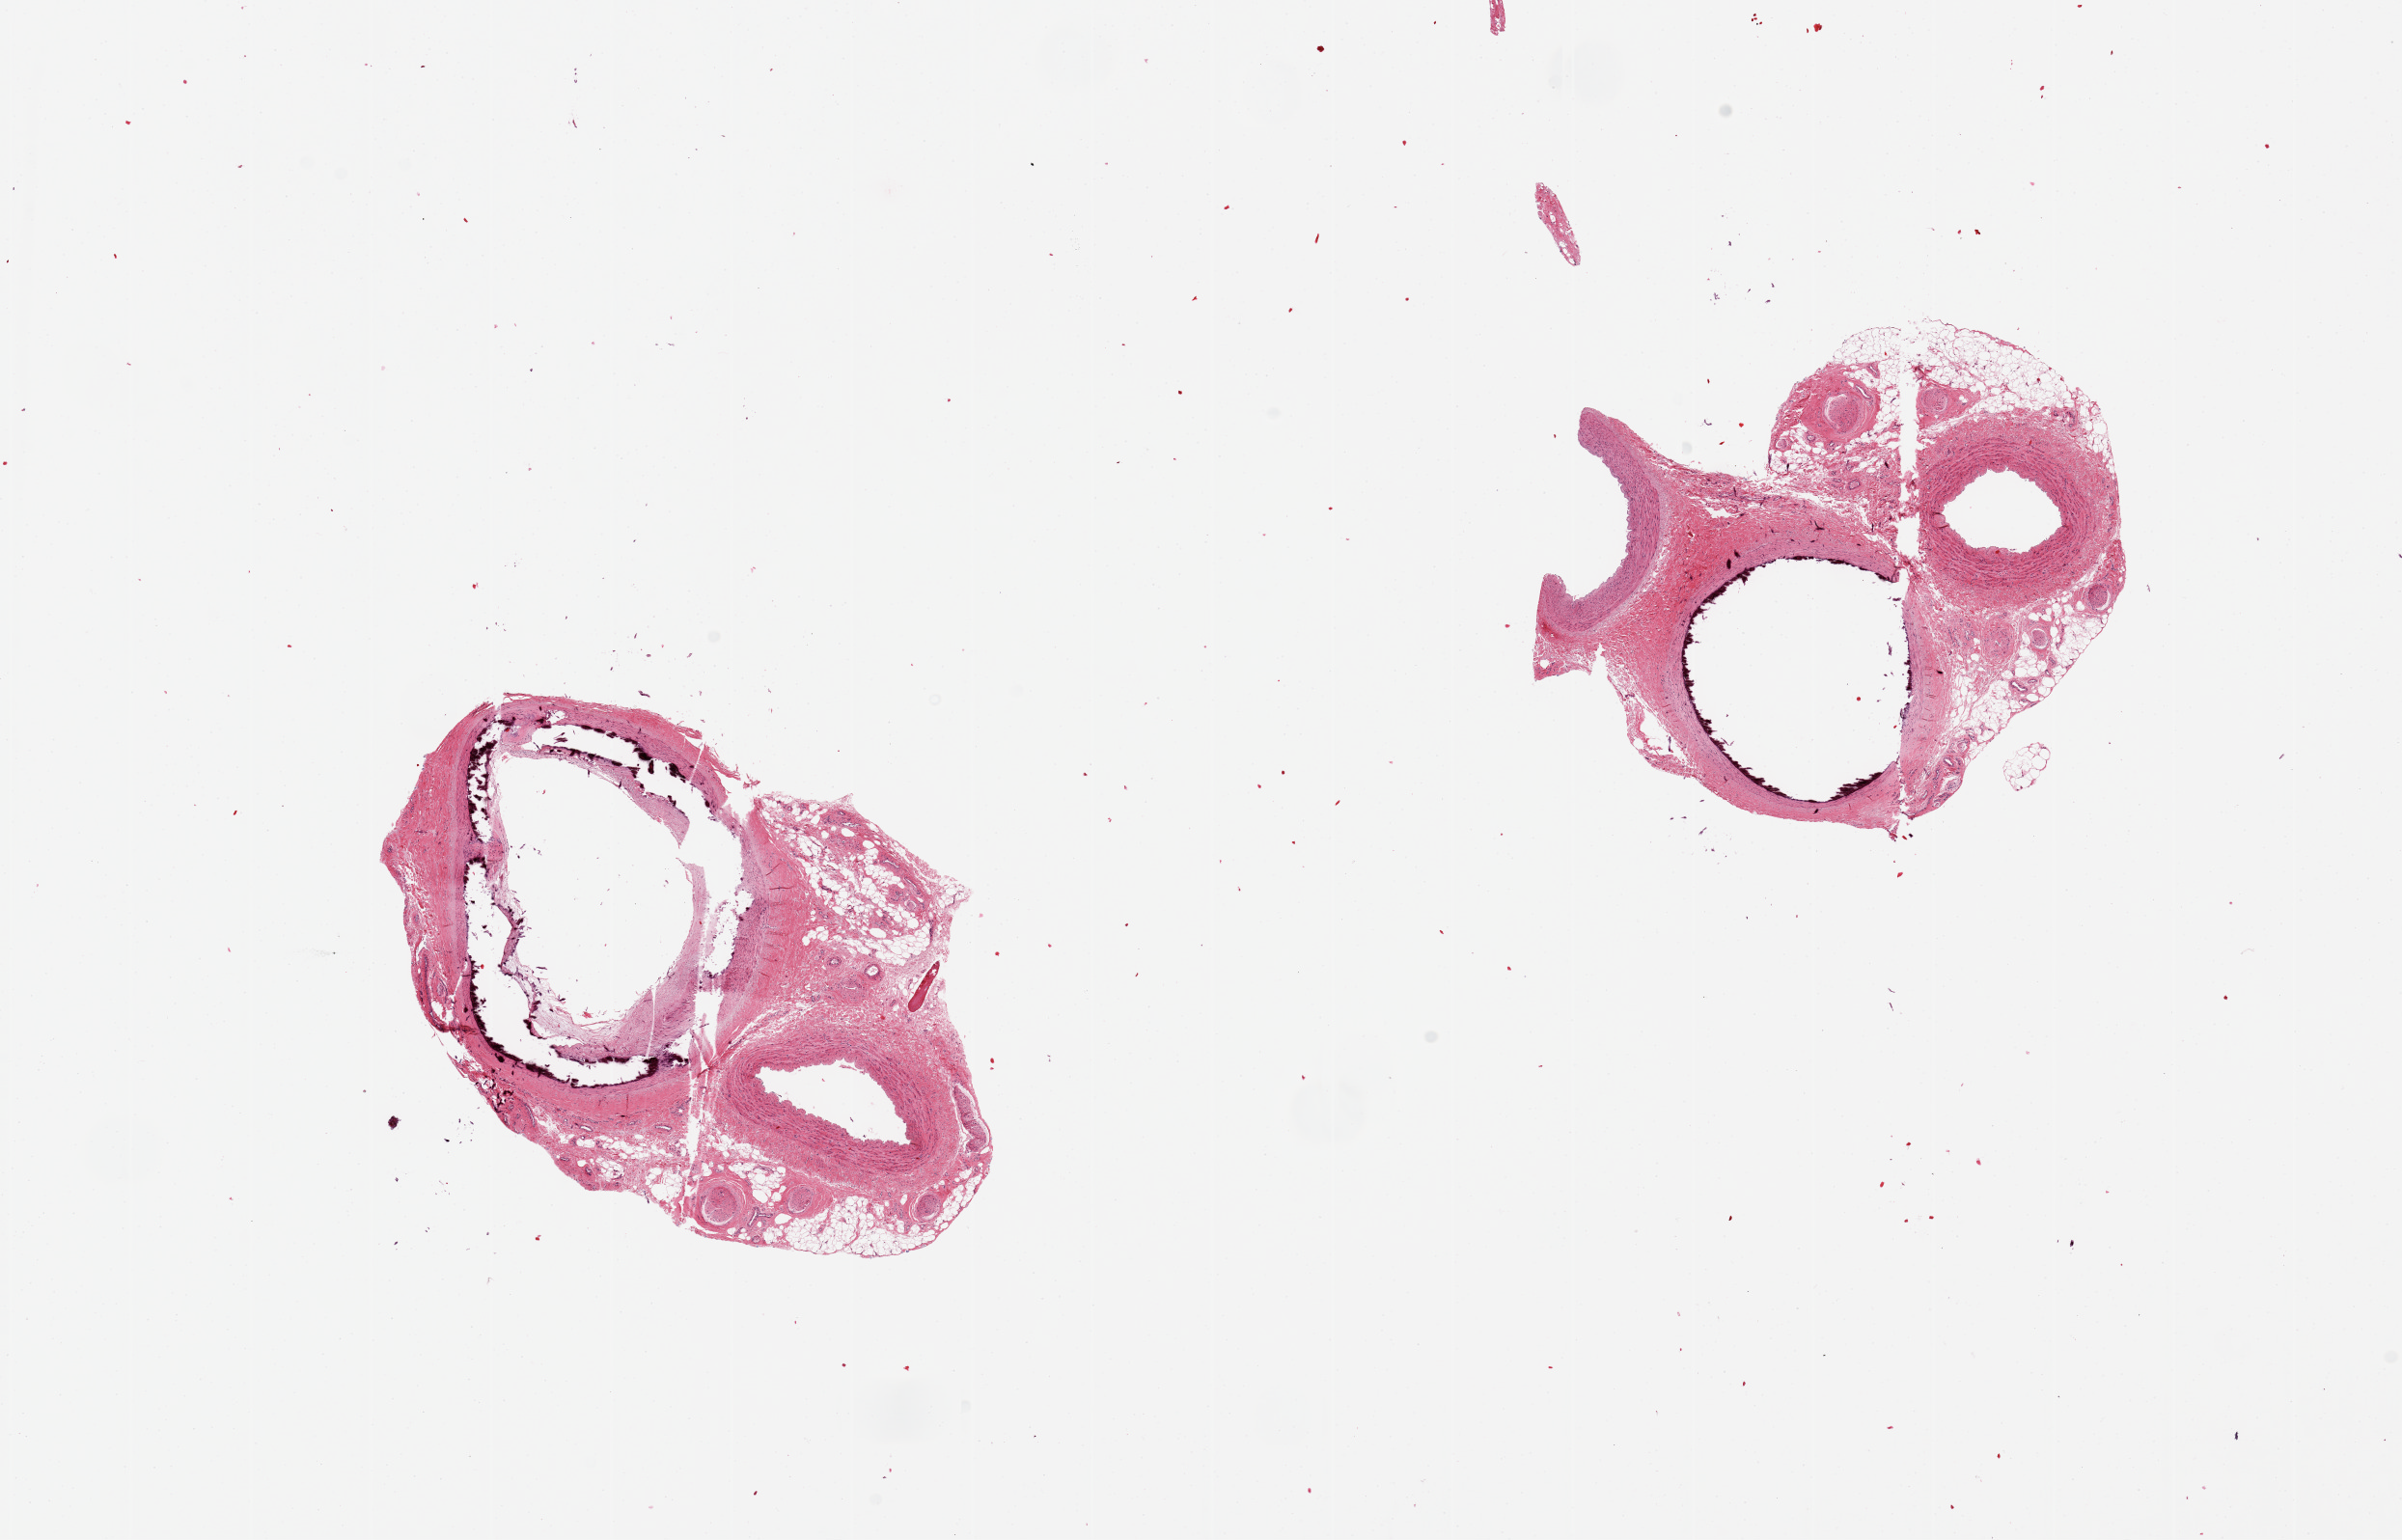
Hematoxylin and eosin (H&E) whole-slide image, shown as a low-resolution overview of the whole scanned area (about 19.7 x 12.6 mm, from a 20x scan), PAXgene-fixed, paraffin-embedded tissue, target tissue: tibial artery, donor tissue sample. Male donor.
Pathologist's review note for this sample: 2 pieces, calcified atherosclerosis in both, ~20% occlusive; adherent aggregates fat, peripheral nerve, fibrous tissue up to ~1x2mm; Multiple lumina.